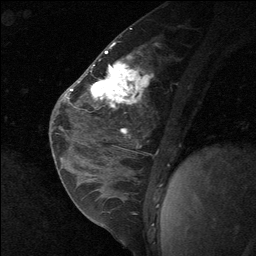
Breast MRI (dynamic contrast-enhanced), one sagittal slice; position 31 of 64 along the scan axis; dynamic contrast-enhanced study with each time point stored as its own series, time point 2 of 3 at this slice position (early post-contrast, ordered by acquisition time); 1.5 T; TE 4.8 ms, TR 27 ms; 2 mm slice thickness; 256 × 256 image matrix, field of view 180 × 180 mm. Patient: female, 26 years. From the clinical record (not read from this slice): setting: breast cancer imaged before/during neoadjuvant chemotherapy; receptor status: HR-positive, HER2-negative.
Structures marked on this image (semi-automatically segmented with operator editing):
- analysis volume of interest (the breast-tissue region the enhancement analysis was run in; not a lesion): box from (x=86, y=43) to (x=127, y=138) px
- tumour enhancement mask (voxels above the 90 % enhancement threshold inside the analysis volume of interest): (x=91, y=66)–(x=119, y=99)